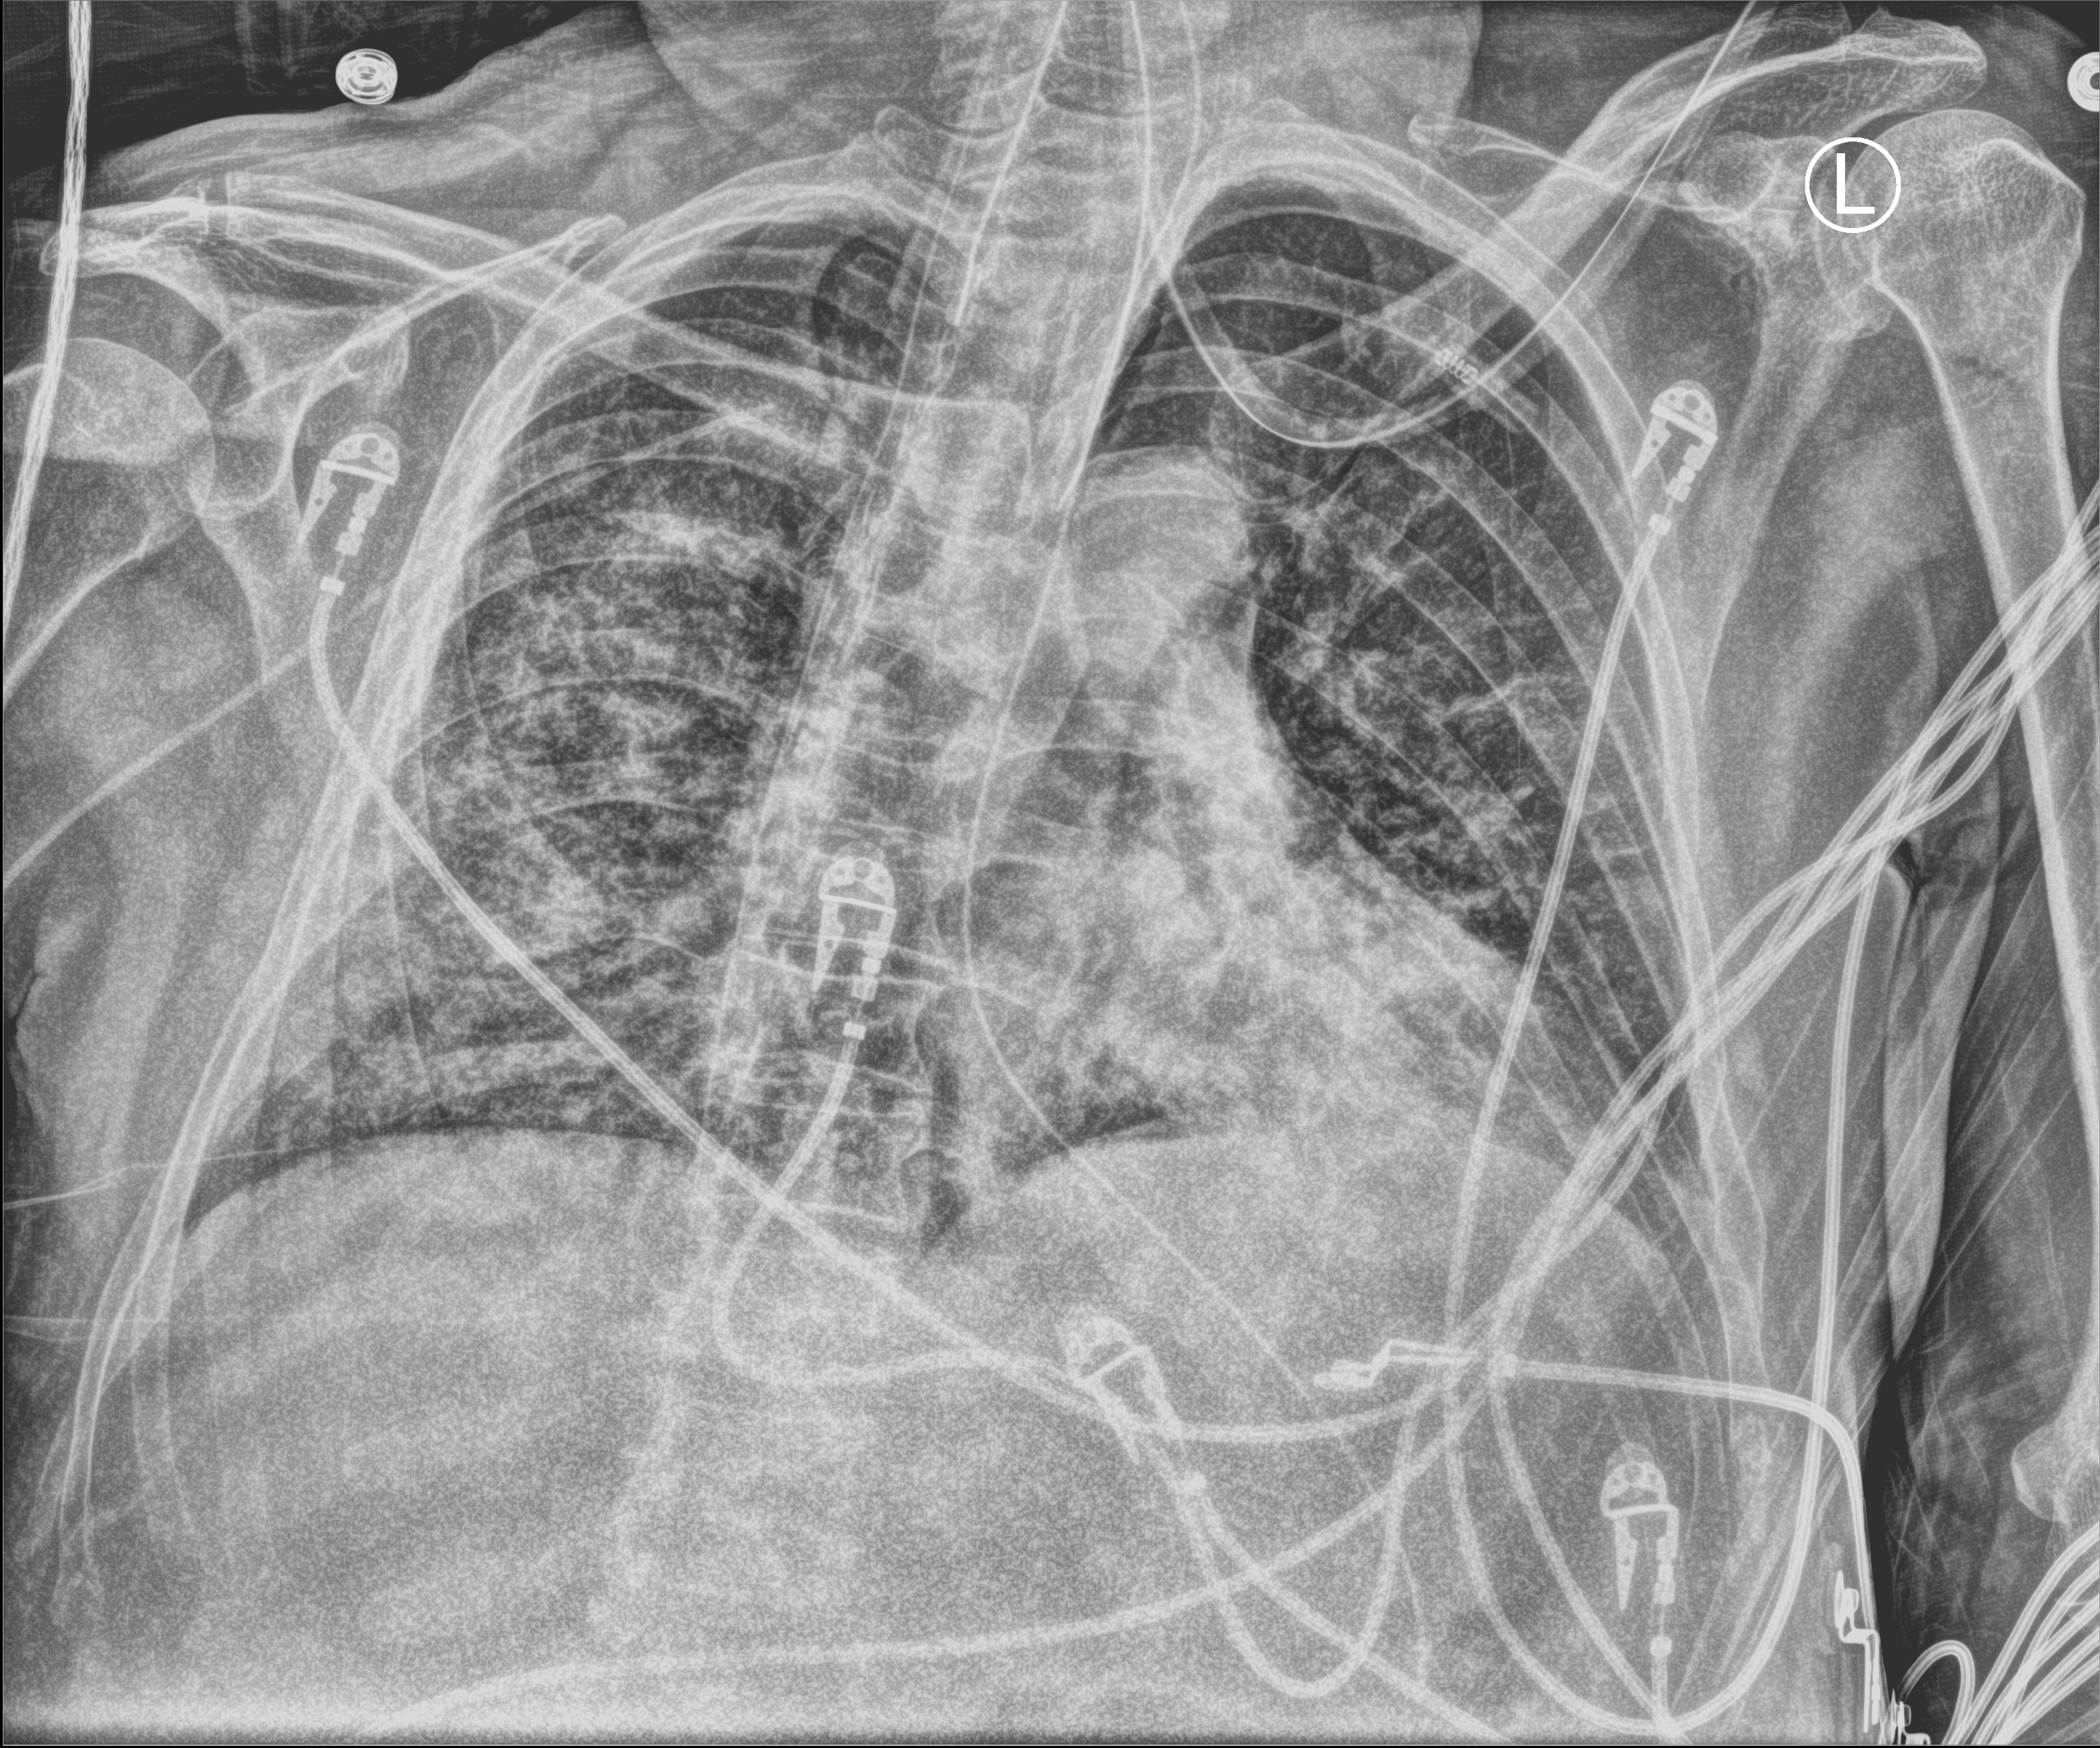
Portable chest radiograph. Male patient hospitalised with COVID-19, age 60–74 years.
From the hospital-stay record, not from the radiograph (when in the stay this image was taken is not recorded):
- other chronic lung disease (admission record): no